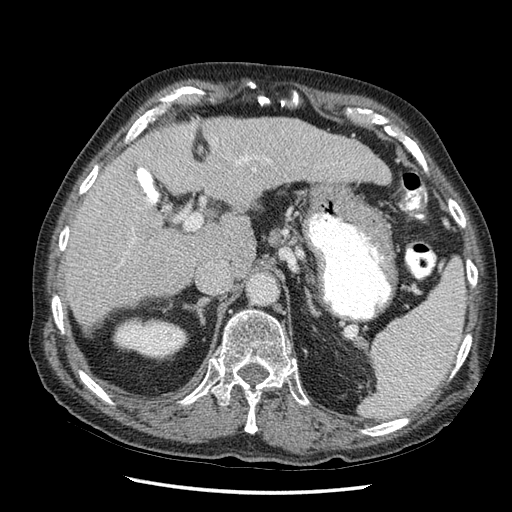
Contrast-enhanced abdominal CT (liver protocol), one axial slice; position 28 of 67 along the scan axis; soft-tissue window (W 400 / L 40 HU); 2.5 mm slice thickness; 512 × 512 image matrix, field of view 360 × 360 mm. Case-level facts recorded for this patient, not image findings: diagnosis: hepatocellular carcinoma (patient treated with transarterial chemoembolisation; whether this scan precedes or follows treatment is not stated here); TNM stage (as recorded): Stage-I; Child-Pugh class: A; tumour differentiation: moderately differentiated; tumour nodularity: uninodular.
Outlined on this slice (semi-automatic segmentation, software-assisted and operator-edited):
- liver parenchyma outside the tumour (the mass and vessels are separate outlines, so this box may not span the whole liver): bounding box [x1, y1, x2, y2] px = [64, 118, 390, 318]
- liver vessels: [98, 157, 332, 246]